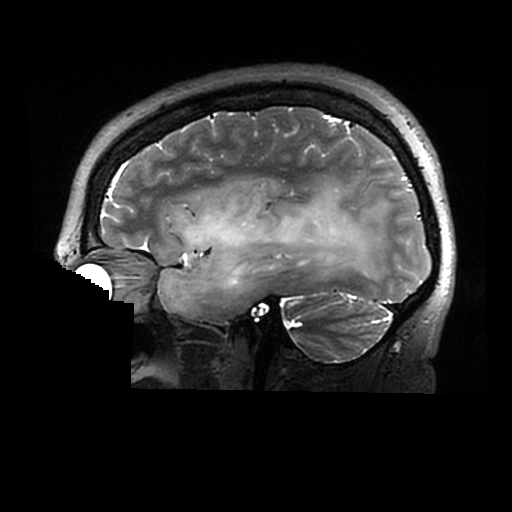
Brain MRI from a brain-tumour surgery series, one sagittal slice; slice 210 of 320 in the series (ordered by position); 0.6 mm slice thickness; 512 × 512 image matrix, field of view 240 × 240 mm. From the clinical record (not read from this slice): histopathology: Astrocytoma; WHO grade: 2; IDH mutation: yes.
Structures marked on this image (expert manual segmentation):
- tumour: box from (x=158, y=179) to (x=385, y=312) px